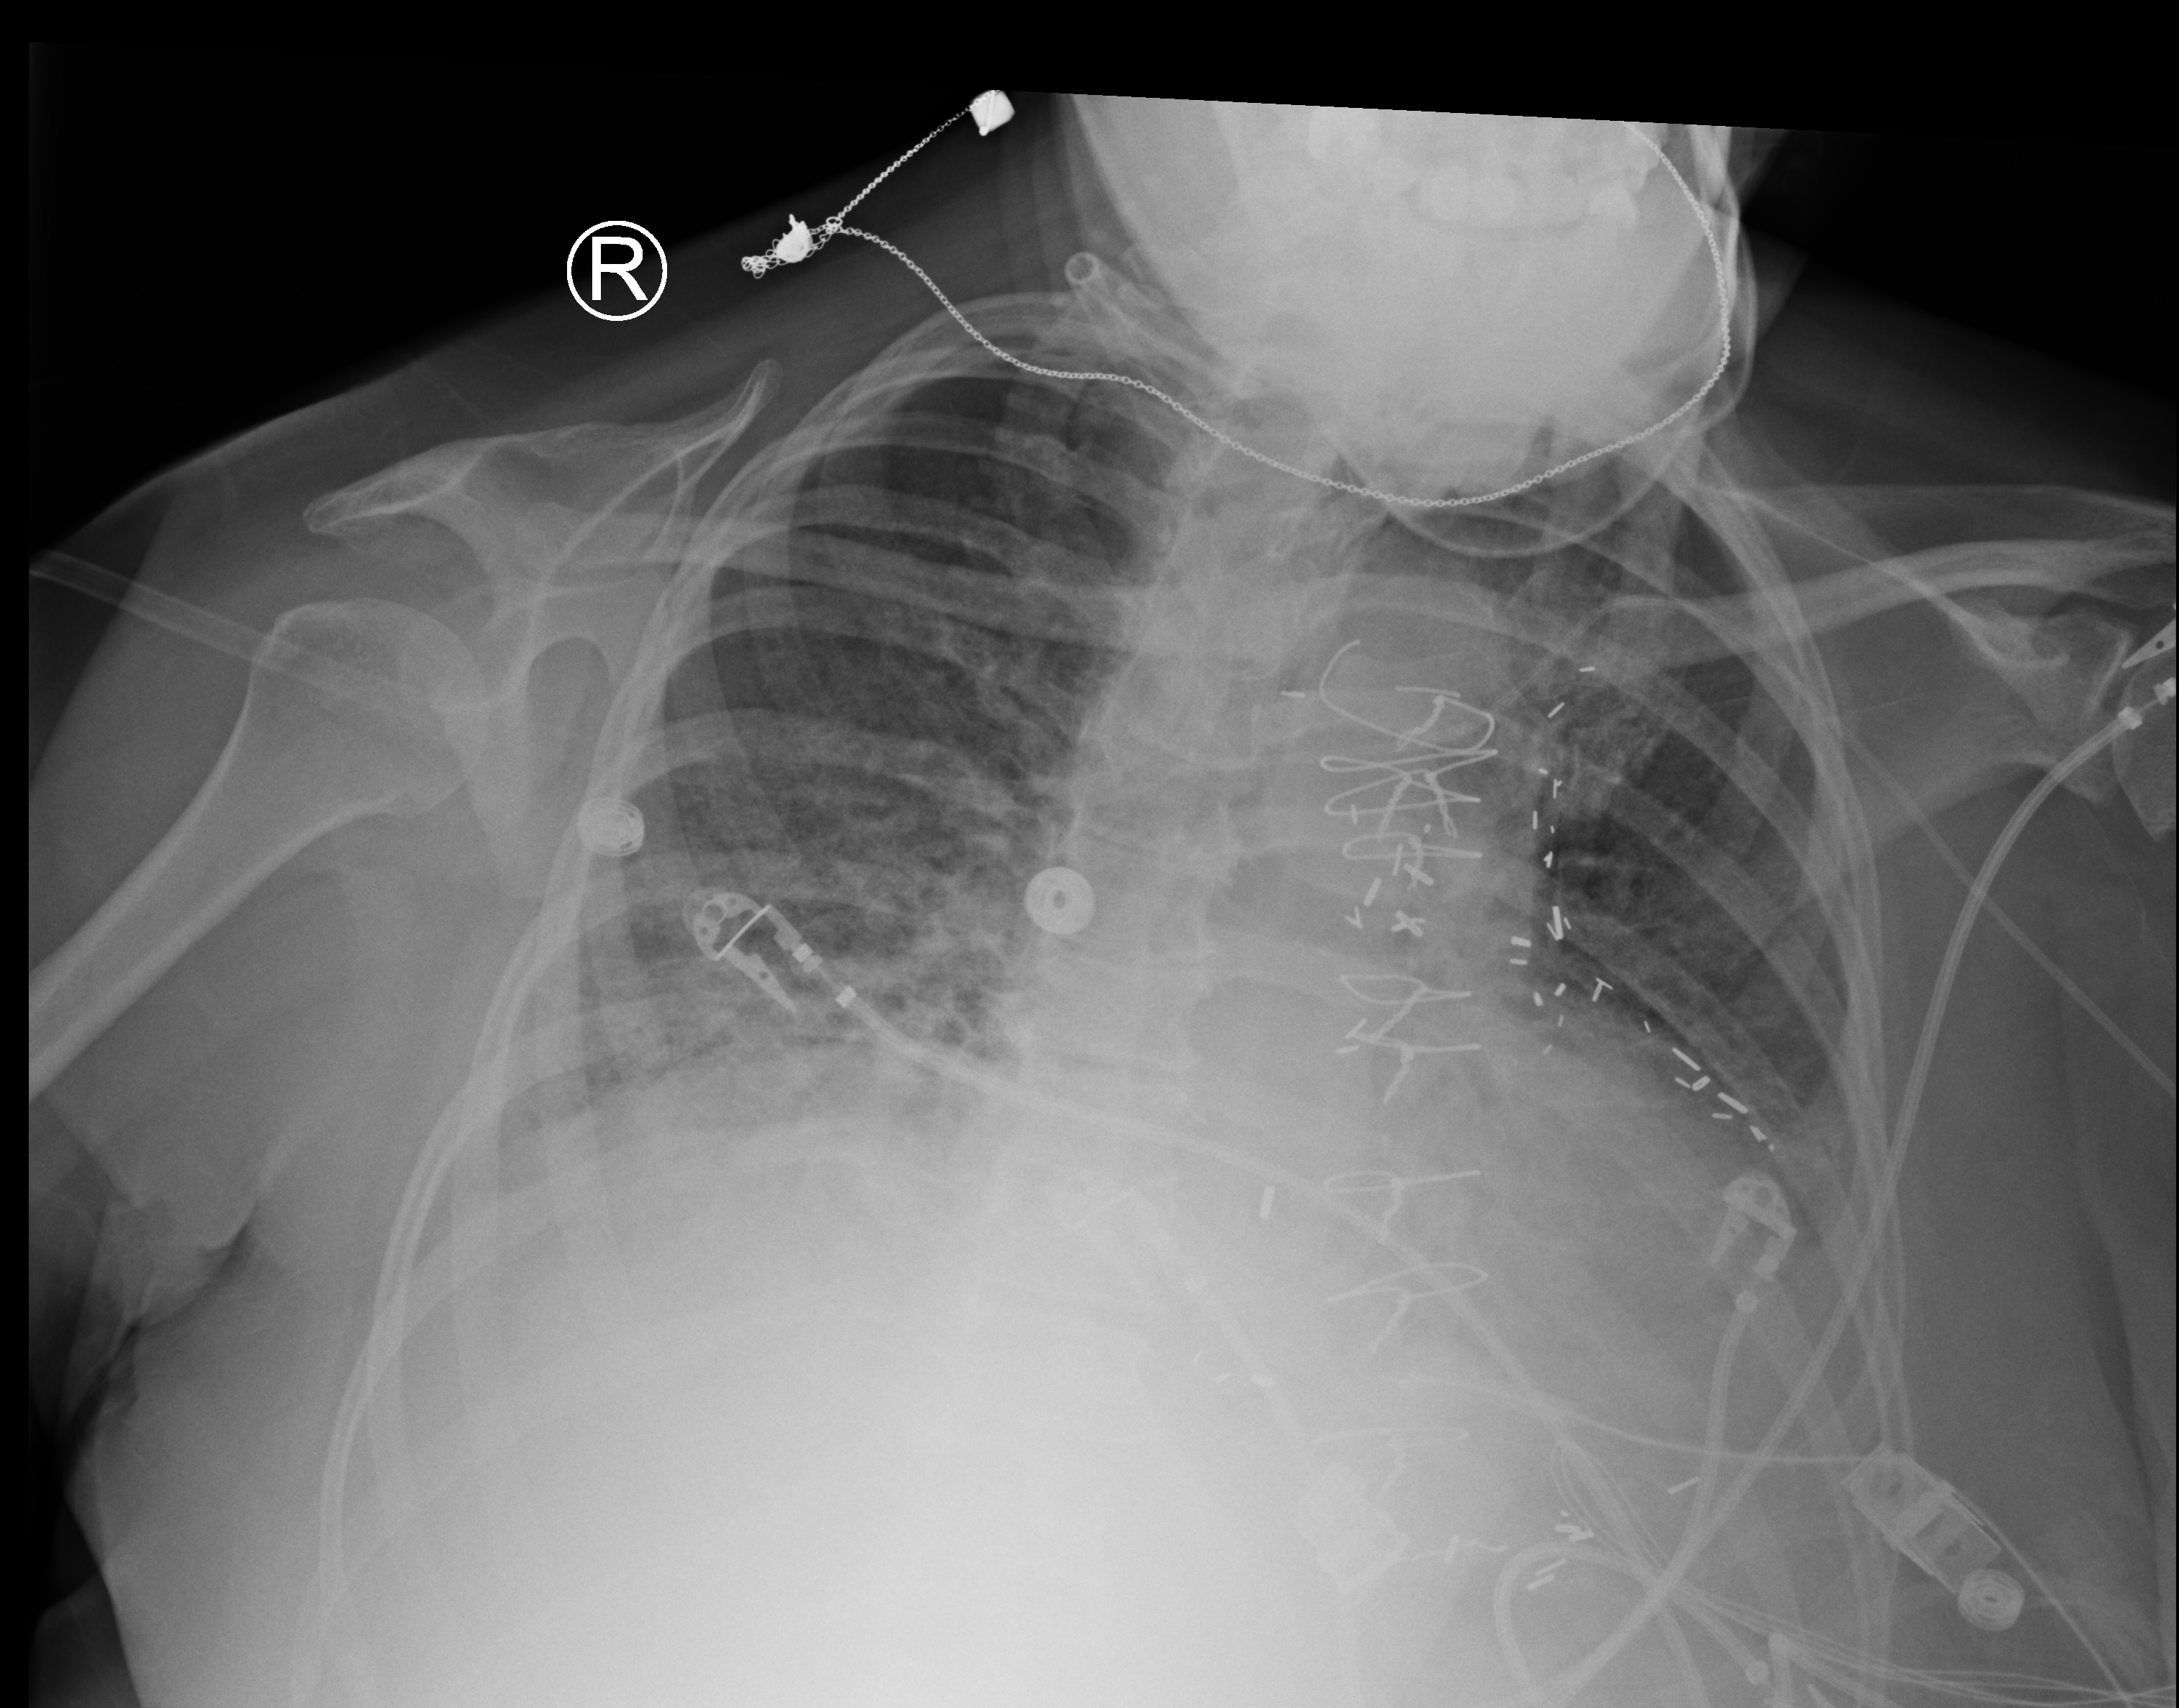
Portable chest radiograph. Patient hospitalised with COVID-19; female, aged 60–74 years.
Hospital-stay facts (about this admission, not read from this image; timing relative to this image not recorded): mechanically ventilated during this hospital stay: yes.